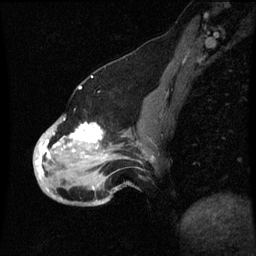
Breast MRI (dynamic contrast-enhanced), one sagittal slice. Slice 23 of 60 in the series (ordered by position). Dynamic contrast-enhanced series, image 2 of 3 at this slice position (ordered by acquisition). 1.5 T. TE 4.2 ms, TR 8.9 ms. 2 mm slice thickness. 256 × 256 image matrix, field of view 200 × 200 mm. Female patient, age 49 years. From the clinical record (not read from this slice): setting: breast cancer imaged before/during neoadjuvant chemotherapy; receptor status: HR-positive, HER2-negative.
Outlined on this slice (semi-automatically segmented with operator editing):
- analysis volume of interest (the breast-tissue region the enhancement analysis was run in; not a lesion): bounding box <34,114,149,199> (left, top, right, bottom; pixels)
- tumour enhancement mask (voxels above the 70 % enhancement threshold inside the analysis volume of interest): <38,124,105,179>